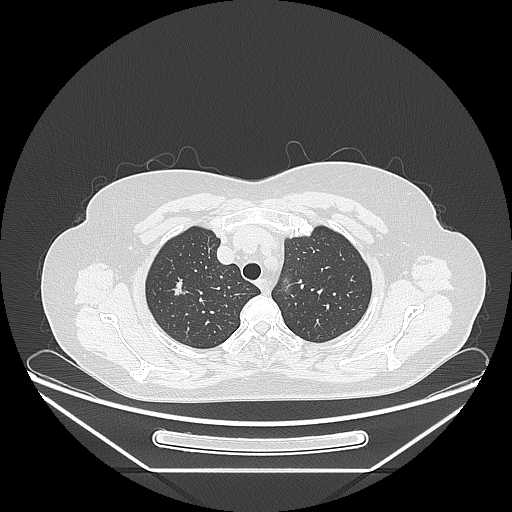
Chest CT, one axial slice; slice 200 of 236 in the series (ordered by position); lung window (W 1500 / L -600 HU); 1.25 mm slice thickness; 512 × 512 image matrix, field of view 433 × 433 mm. Female patient, age 60 years. From the clinical record (not read from this slice): clinical TNM (as recorded): T1c N0 M0; histopathological grade: G2-3.
Outlined on this slice (rectangle marked by the reading radiologist):
- lung tumour (recorded histology: adenocarcinoma): bounding box [x1, y1, x2, y2] px = [165, 271, 188, 302]